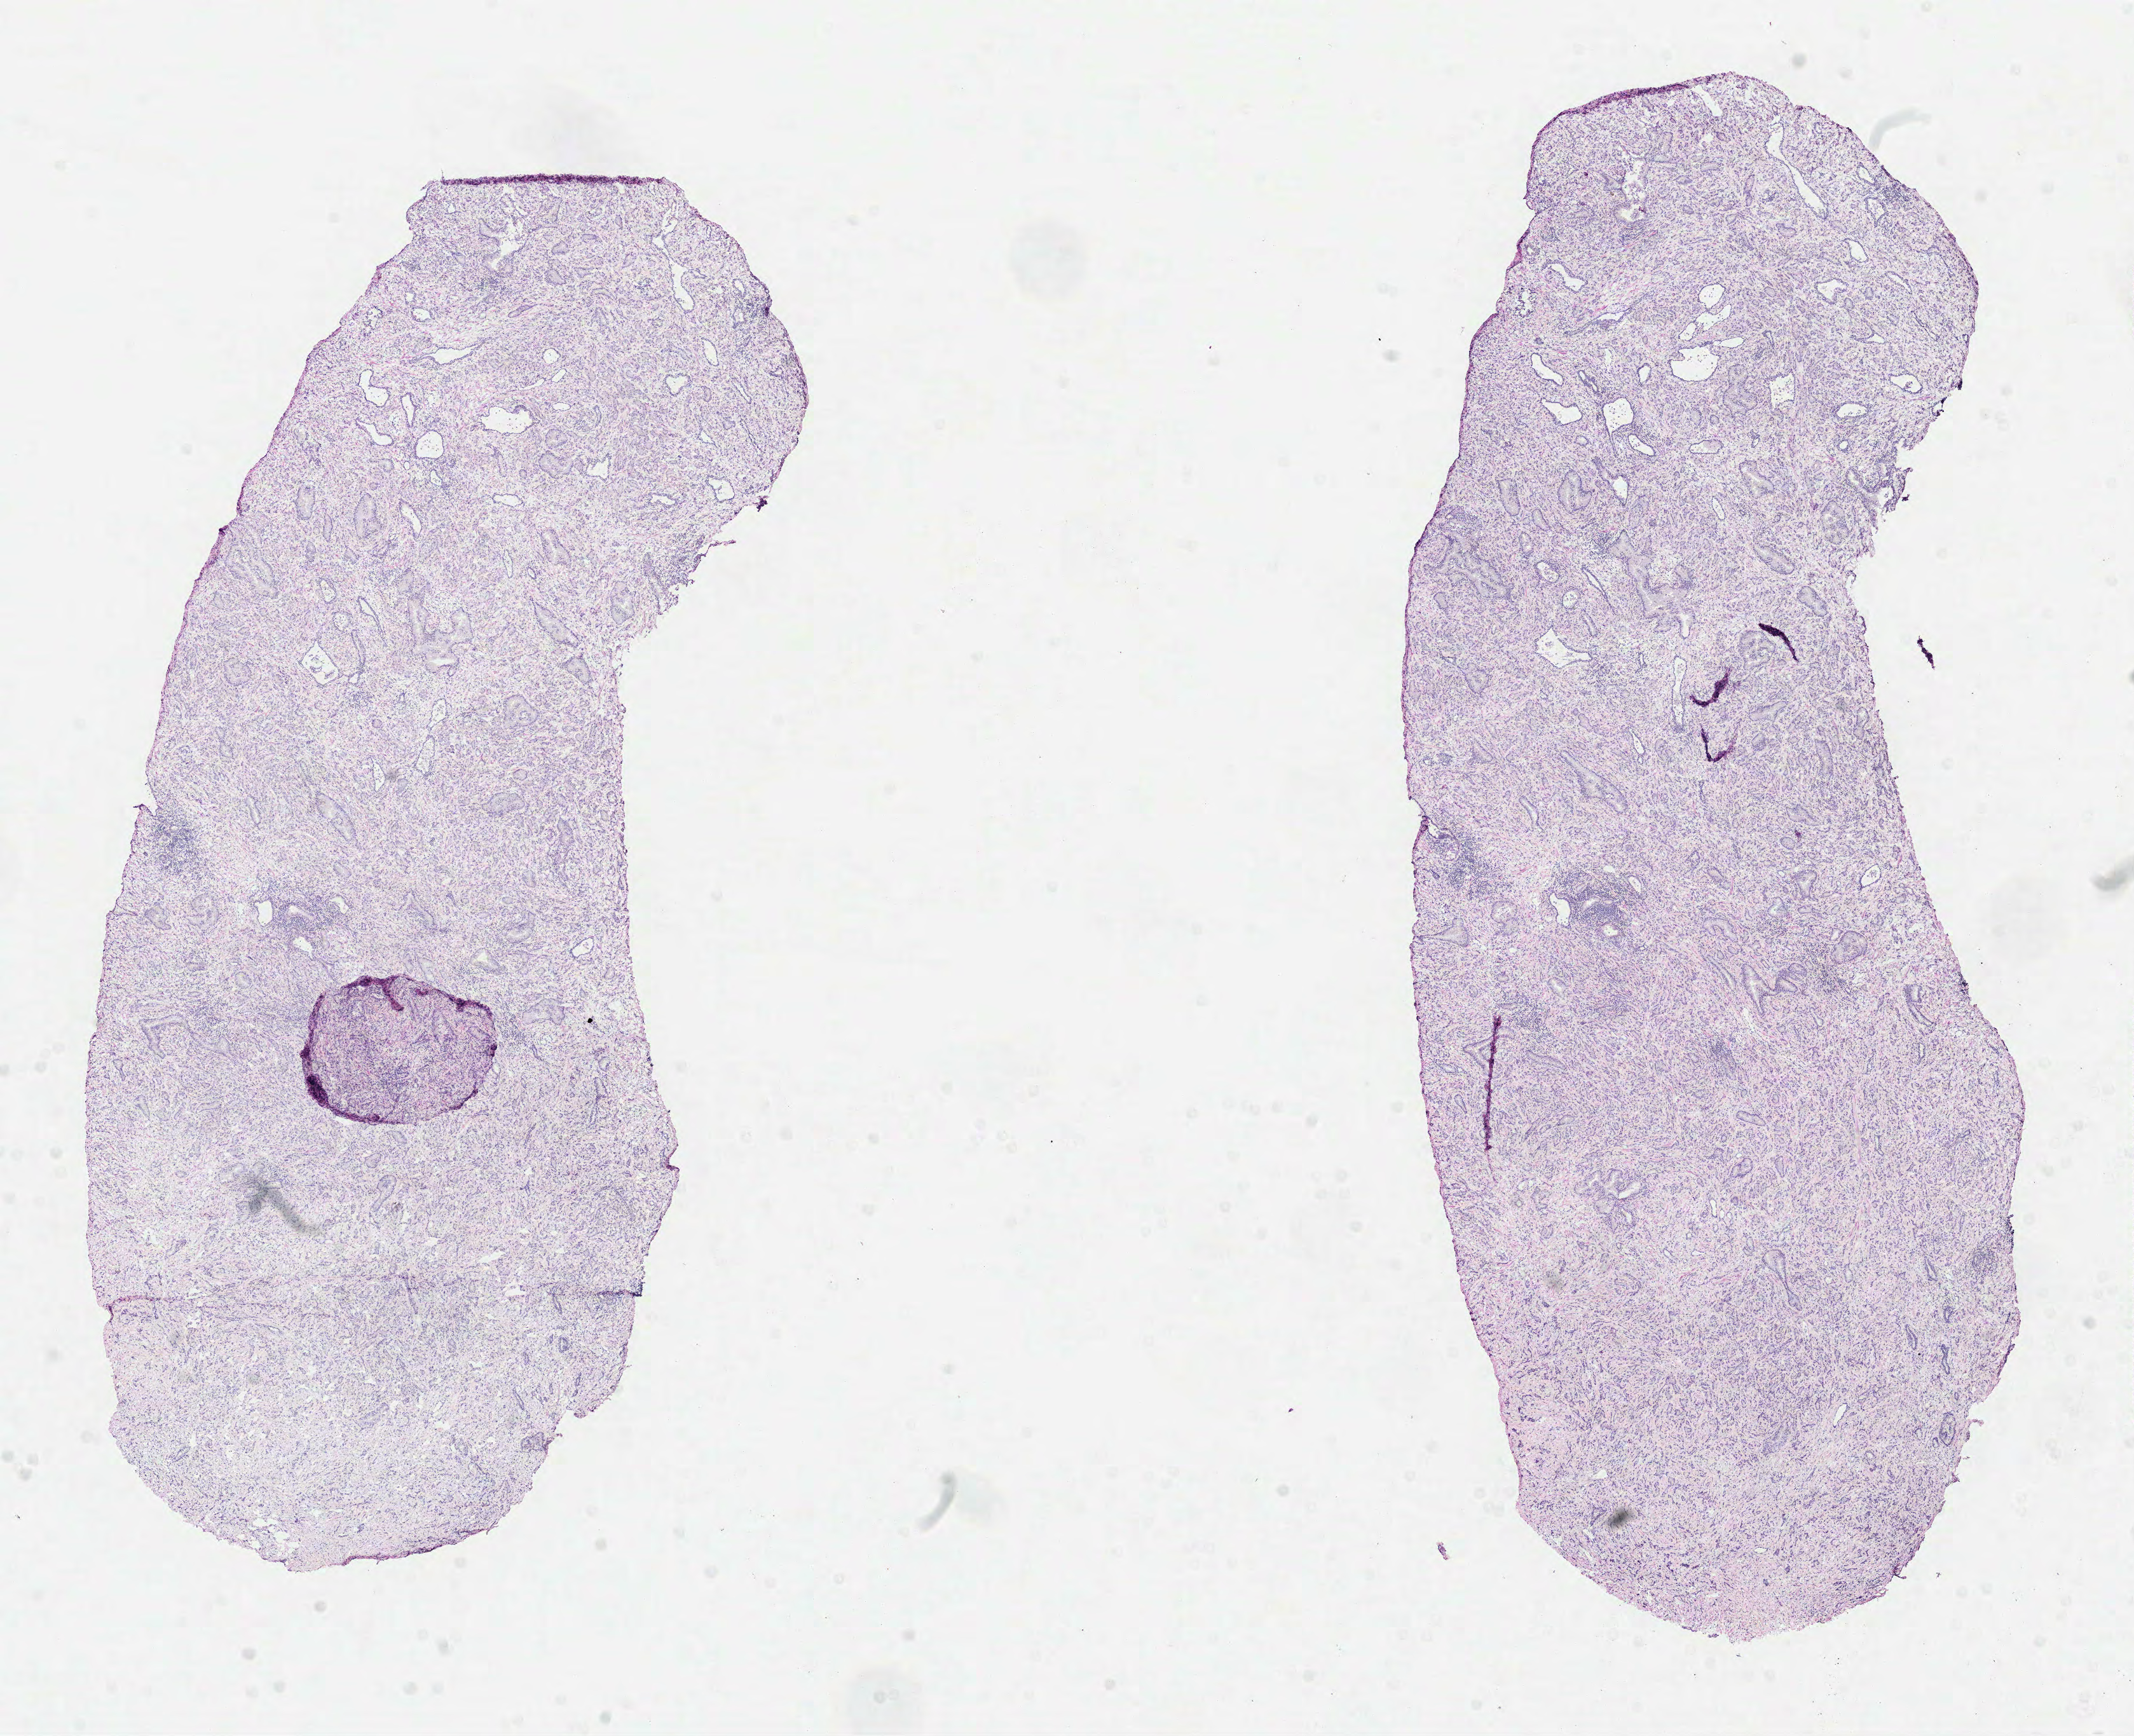
Hematoxylin and eosin (H&E) stained whole-slide image — a low-resolution overview of the entire scanned area, about 13.5 x 11.0 mm (slide scanned at 40x). Formalin-fixed paraffin-embedded (FFPE) diagnostic section. Prostate, primary tumour sample. Male patient; age at initial diagnosis 48 years. Gleason score: 9 (5+4).
Histologic diagnosis: Acinar cell carcinoma (prostate gland). Lymph nodes positive (case pathology): 0 of 8 examined.